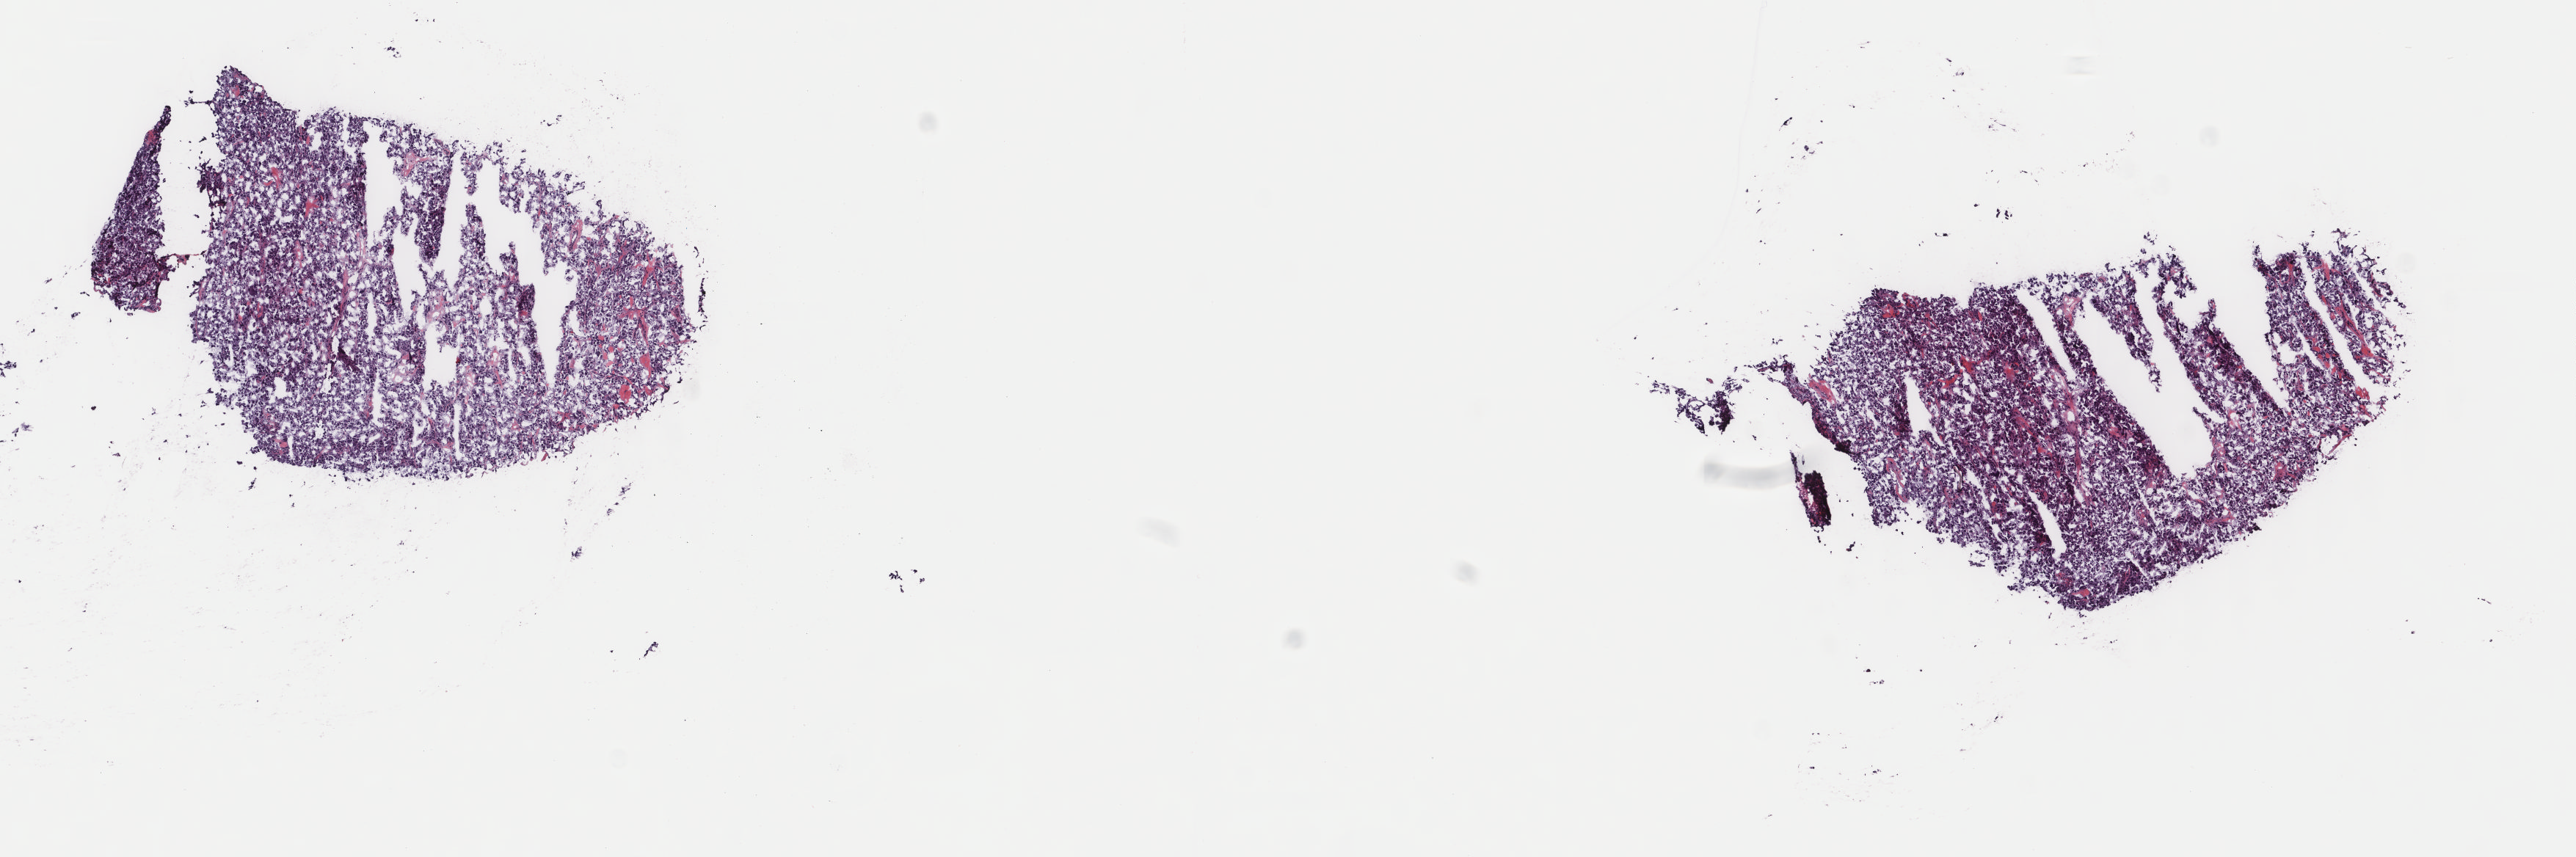
Hematoxylin and eosin (H&E) stained whole-slide image, a low-resolution overview of the entire scanned area, about 13.9 x 4.6 mm (slide scanned at 40x); frozen section from the top of the tissue portion; adrenal gland, primary tumour sample. Patient: female, age at initial diagnosis 46 years. Slide review estimates, as recorded: tumour cells 100%, tumour nuclei 80%, normal cells 0%, stromal cells 0%, necrosis 0%. Infiltration values recorded for this section: lymphocyte infiltration 1%, monocyte infiltration 0%, neutrophil infiltration 0%.
Histologic diagnosis: Pheochromocytoma, NOS.